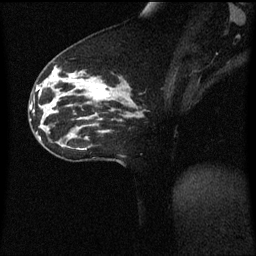
Breast MRI (dynamic contrast-enhanced), one sagittal slice; slice 32 of 60 in the series (ordered by position); dynamic contrast-enhanced series, image 2 of 3 at this slice position (ordered by acquisition); 1.5 T; TE 4.2 ms, TR 8.4 ms; 2 mm slice thickness; 256 × 256 image matrix, field of view 200 × 200 mm. Patient: female, 33 years. Case-level facts recorded for this patient, not image findings: setting: breast cancer imaged before/during neoadjuvant chemotherapy; receptor status: triple-negative.
Annotated regions visible in this slice (semi-automatically segmented with operator editing):
- analysis volume of interest (the breast-tissue region the enhancement analysis was run in; not a lesion): box from (x=76, y=70) to (x=123, y=113) px
- tumour enhancement mask (voxels above the 70 % enhancement threshold inside the analysis volume of interest): (x=82, y=80)–(x=111, y=99)